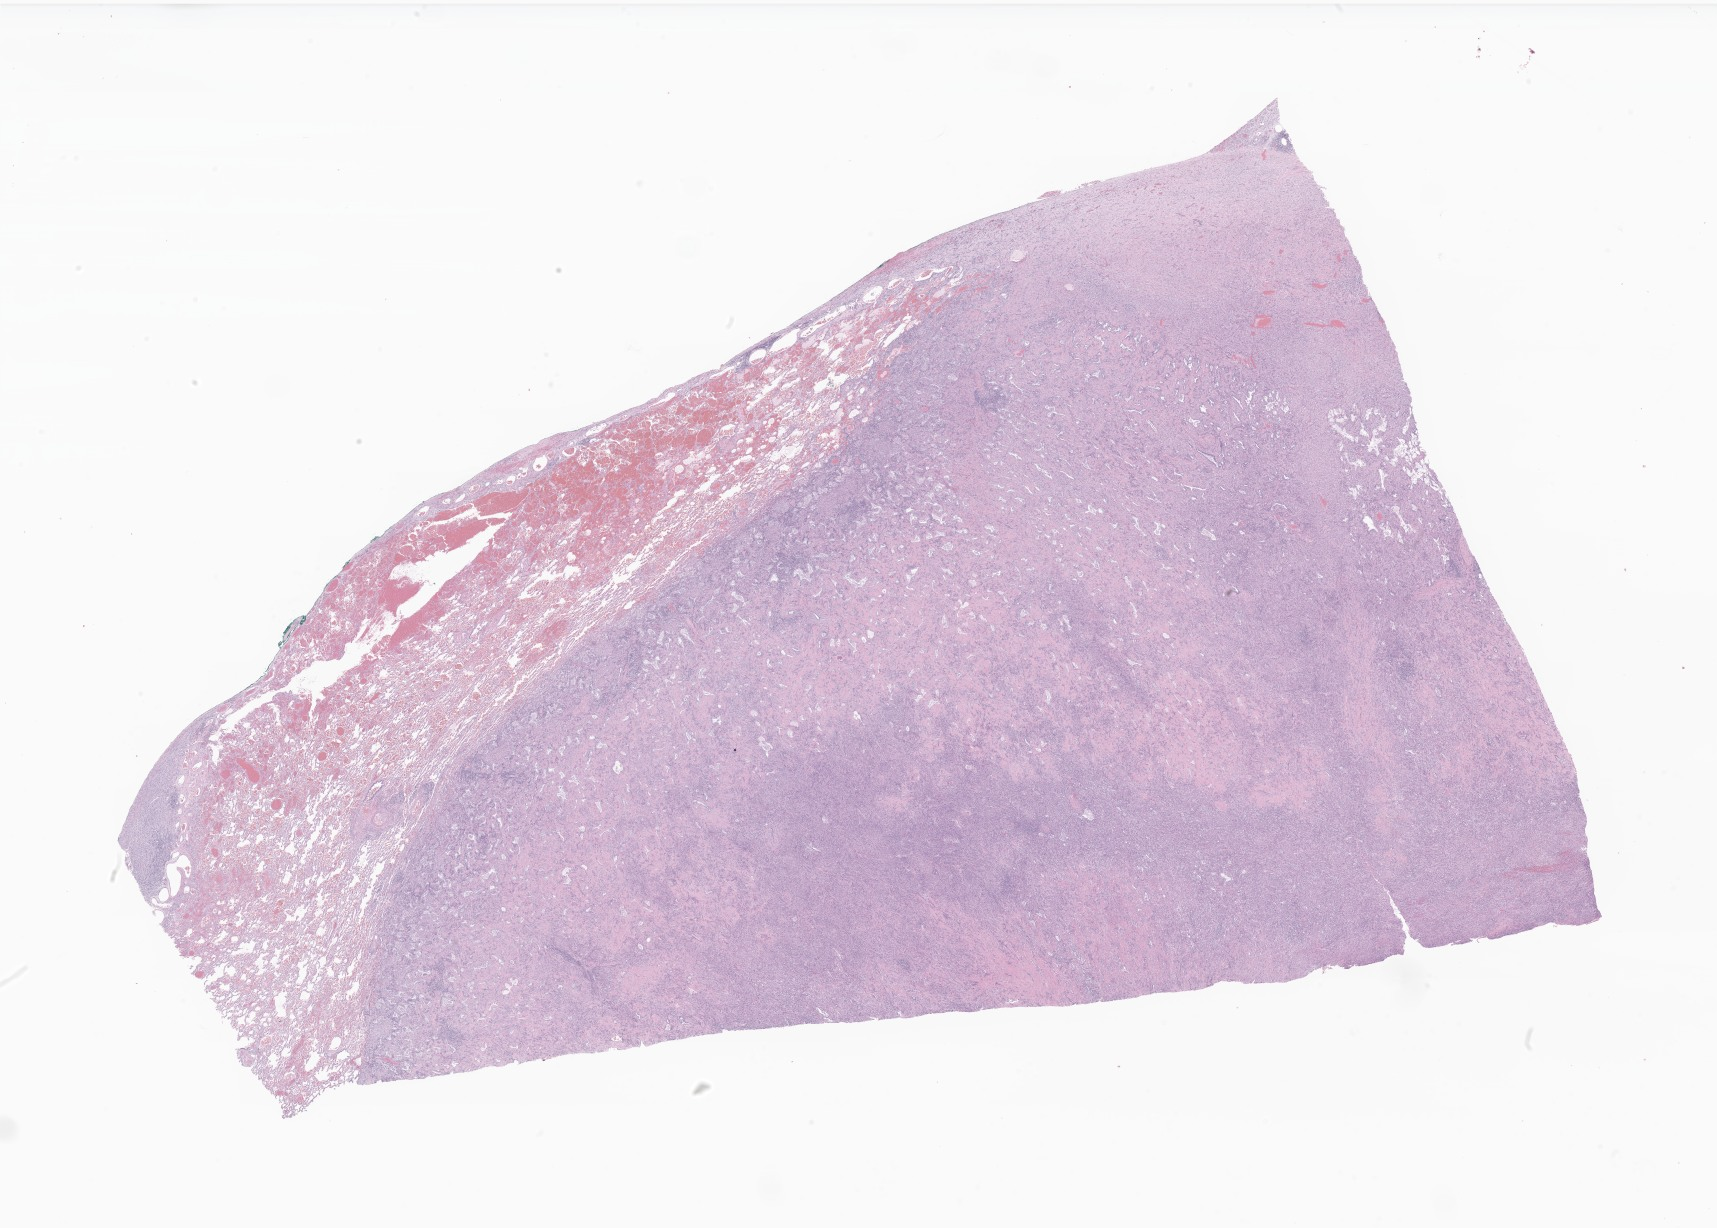
Digitized hematoxylin and eosin (H&E)-stained section of tumor tissue from the lower lobe of lung — whole scanned area (about 29.0 x 20.7 mm) shown as a low-resolution overview; FFPE section. Patient female; age 247 months (20 years 7 months).
* diagnosis: Myofibroblastic tumor, NOS